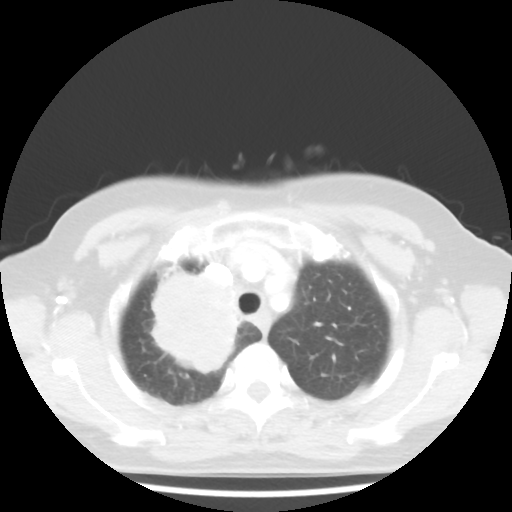
Chest CT, one axial slice; position 36 of 44 along the scan axis; 100 kVp; lung window (W 1500 / L -600 HU); 5 mm slice thickness; 512 × 512 image matrix, field of view 316 × 316 mm. Female patient, age 62 years. Case-level facts recorded for this patient, not image findings: clinical TNM (as recorded): T3 N0 M0.
Structures marked on this image (rectangle marked by the reading radiologist):
- lung tumour (recorded histology: small cell carcinoma): bounding box (x1, y1, x2, y2) in pixels: (137, 259, 247, 379)